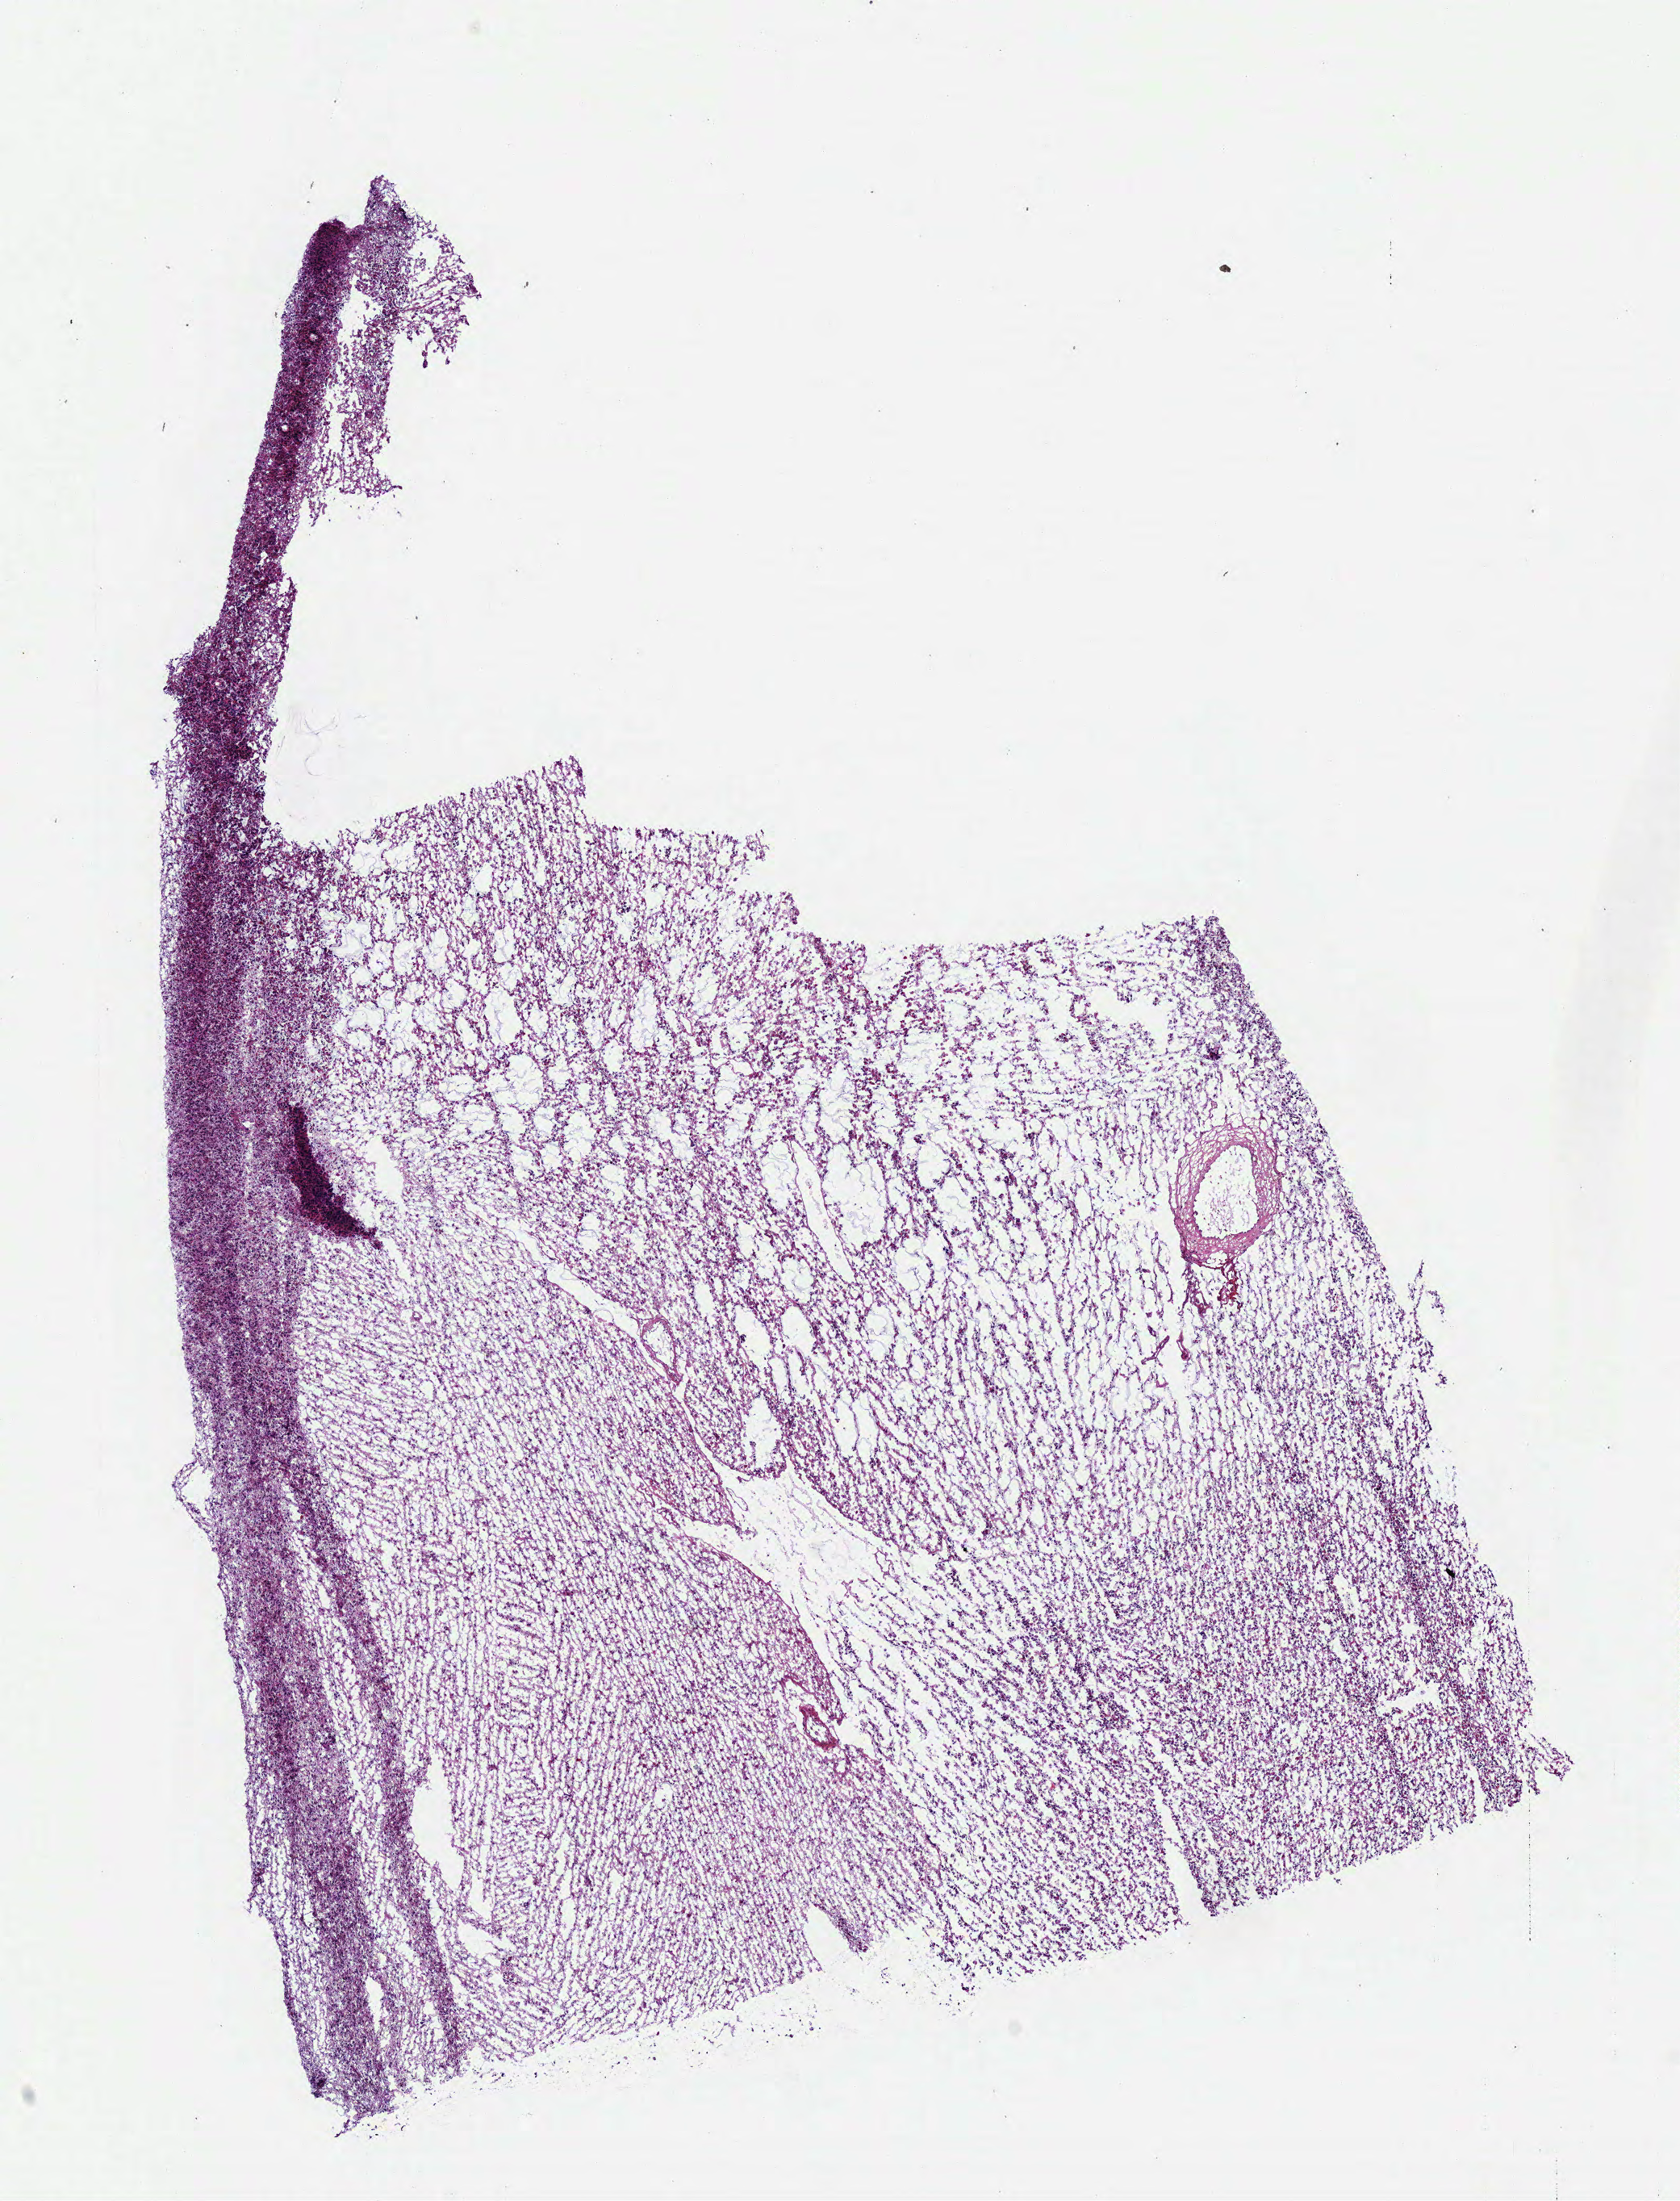
Hematoxylin and eosin (H&E) stained whole-slide image, shown as a low-resolution overview of the whole scanned area (about 8.2 x 10.7 mm, slide scanned at 40x); frozen section; brain, primary tumour sample. Female patient; age at initial diagnosis 49 years. Histologic grade: G3 (poorly differentiated). Composition of this section per pathologist review: tumour cells 100%, tumour nuclei 75%, normal cells 0%, stromal cells 0%, necrosis 0%.
Laterality: right. Pathologic diagnosis: Mixed glioma.